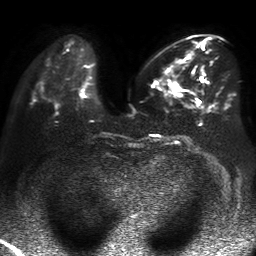
Breast MRI, one axial slice; position 21 of 50 along the scan axis; diffusion-weighted series; image 2 of 4 stored at this slice position (different b-values; order by instance number); 1.5 T; 4 mm slice thickness; 256 × 256 image matrix, field of view 360 × 360 mm. Female patient.
Outlined on this slice (expert manual segmentation):
- tumour on diffusion-weighted imaging: box from (x=169, y=59) to (x=184, y=91) px